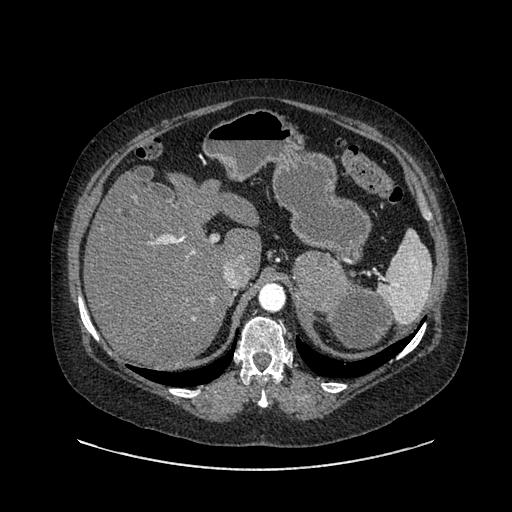
Contrast-enhanced abdominal CT, one axial slice; position 612 of 769 along the scan axis; intravenous contrast given; soft-tissue window (W 400 / L 40 HU); 0.62 mm slice thickness; 512 × 512 image matrix, field of view 460 × 460 mm. Patient: female, 61 years. From the clinical record (not read from this slice): diagnosis: adrenocortical carcinoma; tumour side: left adrenal; tumour size at pathology: 13 cm.
Structures marked on this image (semi-automatically segmented with operator editing):
- mass: bounding box (x1, y1, x2, y2) in pixels: (294, 253, 391, 349)